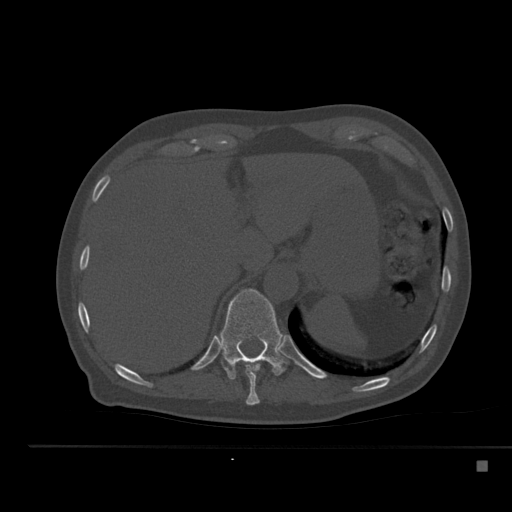
CT including the spine, one axial slice; slice 254 of 517 in the series (ordered by position); 120 kVp; bone window (W 1800 / L 400 HU); 512 × 512 image matrix, field of view 408 × 408 mm. Patient: male, 70 years. Case-level facts recorded for this patient, not image findings: primary cancer: renal; vertebrae with lytic lesions (as recorded): T4, T6, T10, T12, L3, L4, L5.
Outlined on this slice (semi-automatic segmentation, software-assisted and operator-edited):
- T10 vertebra: box from (x=246, y=361) to (x=260, y=405) px
- T11 vertebra: (x=219, y=289)–(x=287, y=380)